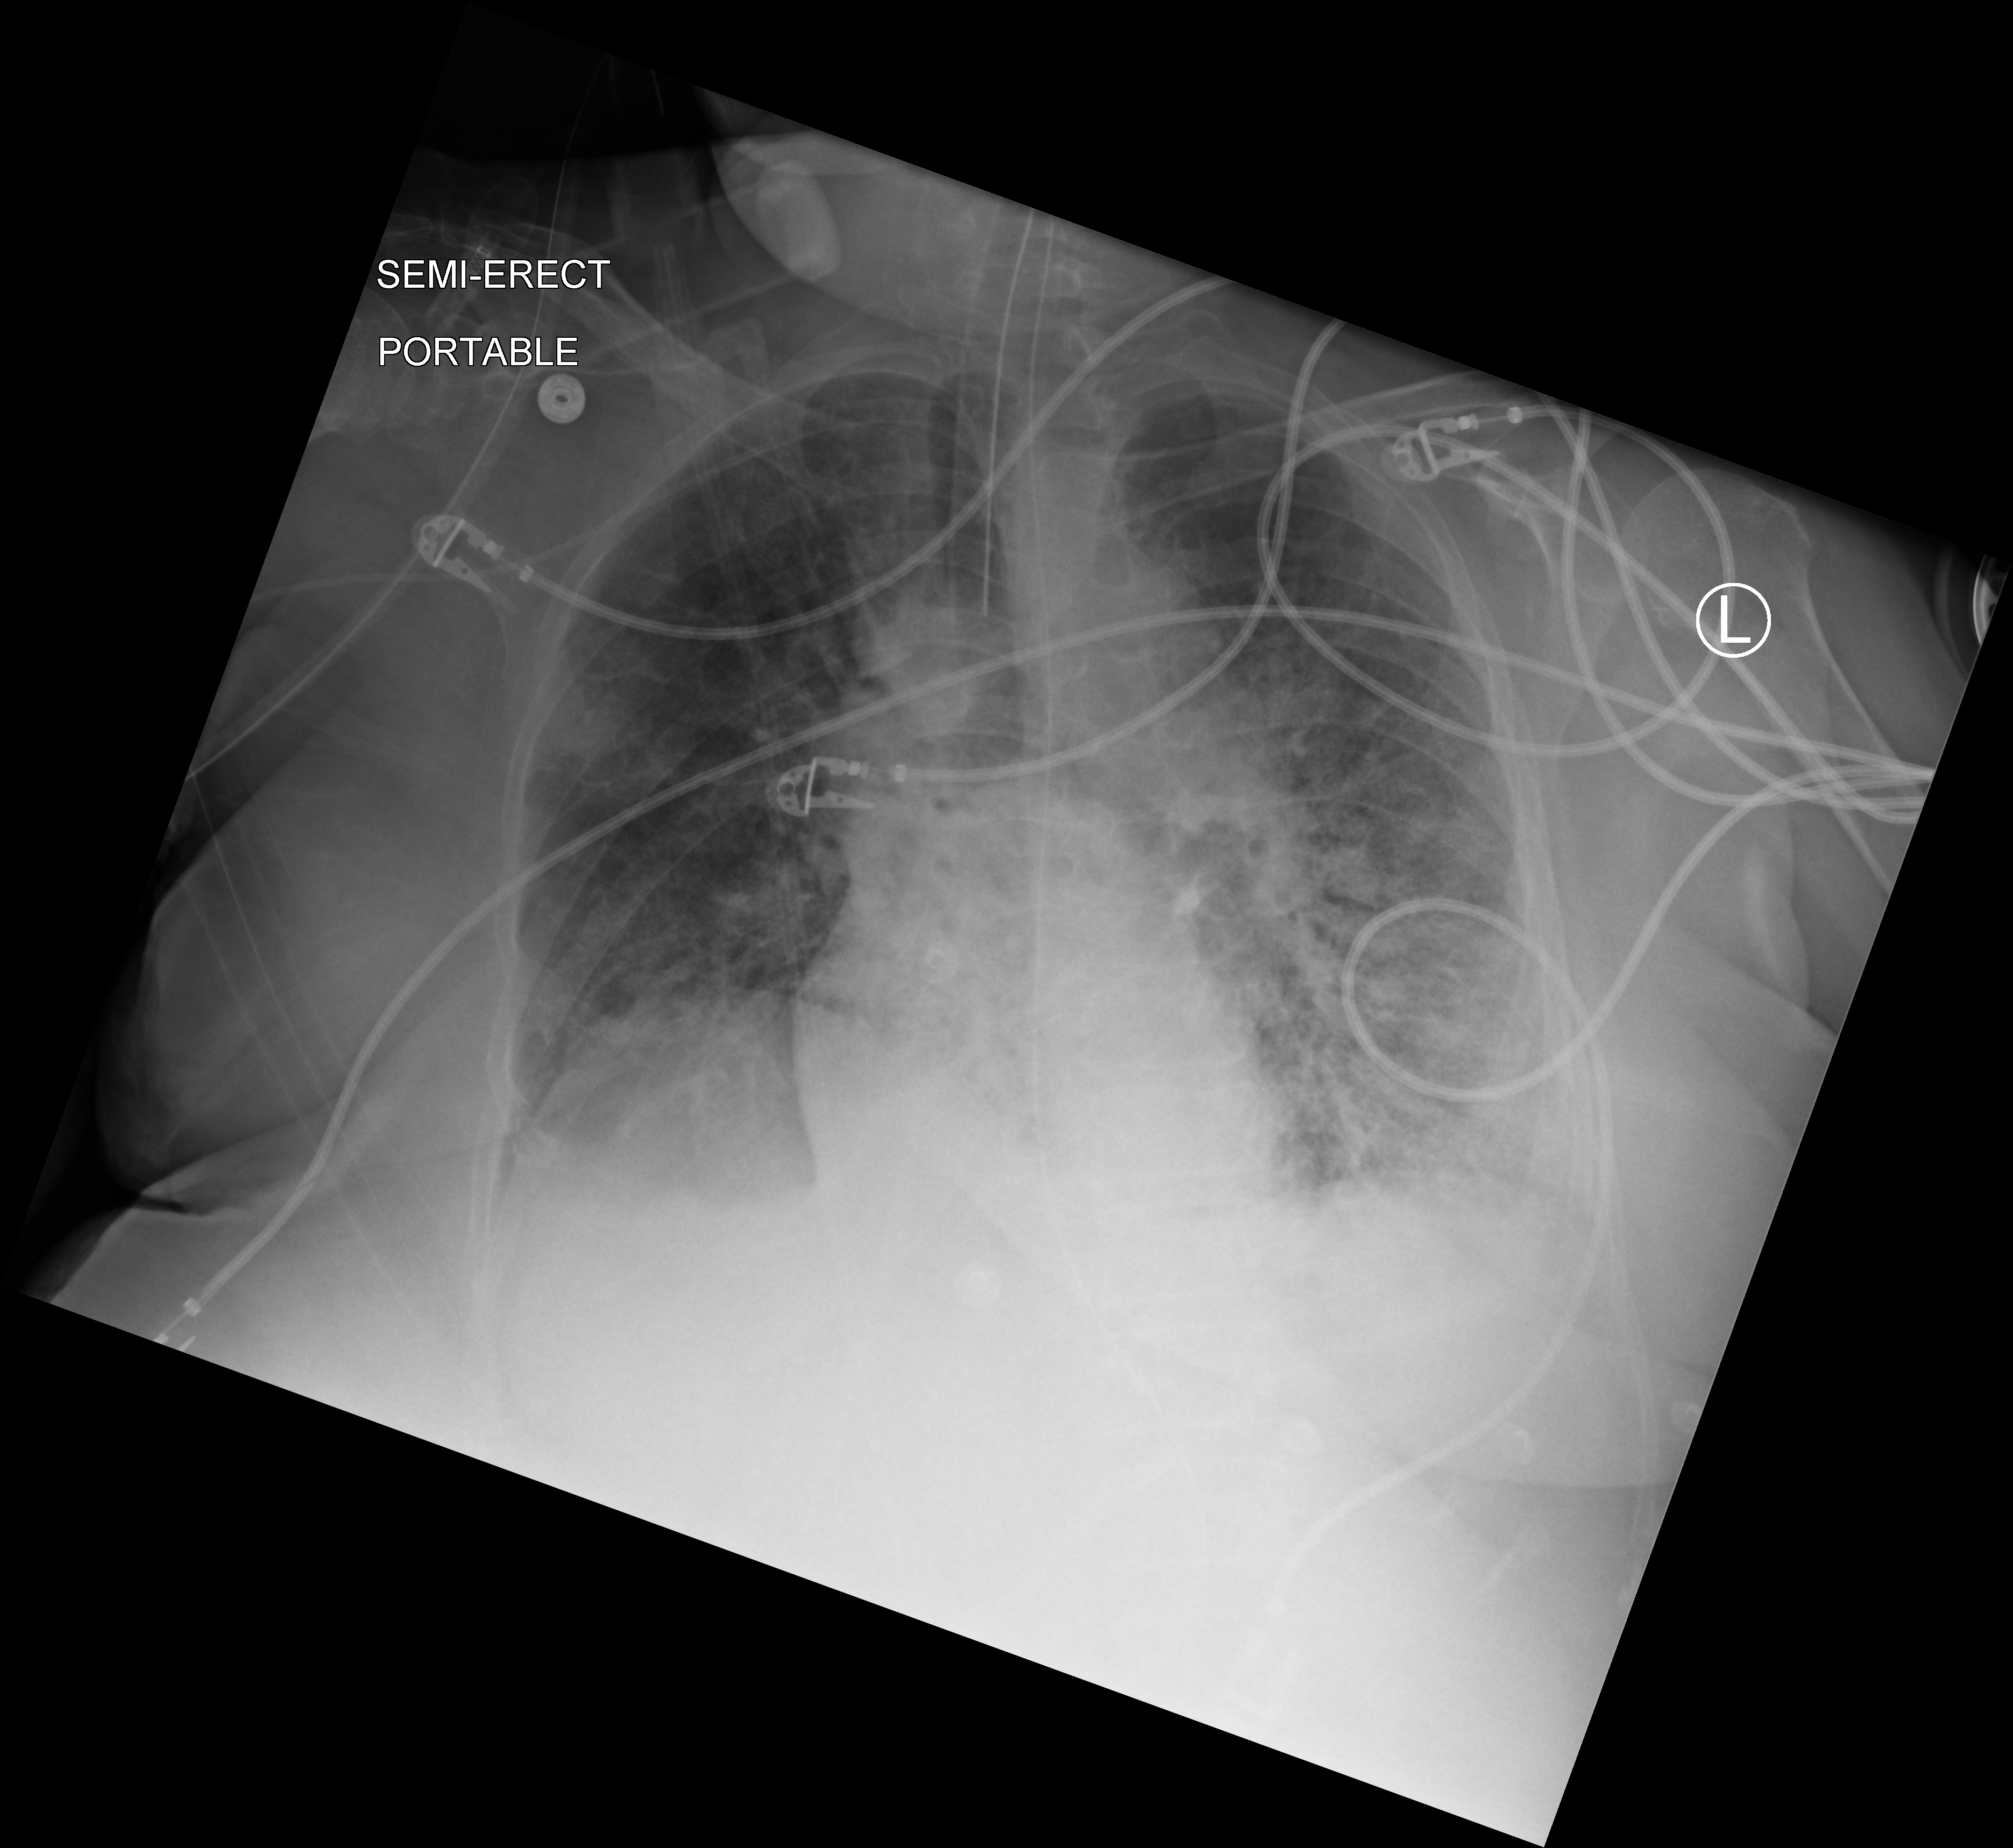
Chest X-ray (portable); anteroposterior (AP) projection. Patient hospitalised with COVID-19; female, aged 60–74 years.
From the hospital-stay record, not from the radiograph (when in the stay this image was taken is not recorded): admitted to intensive care during this hospital stay: yes.